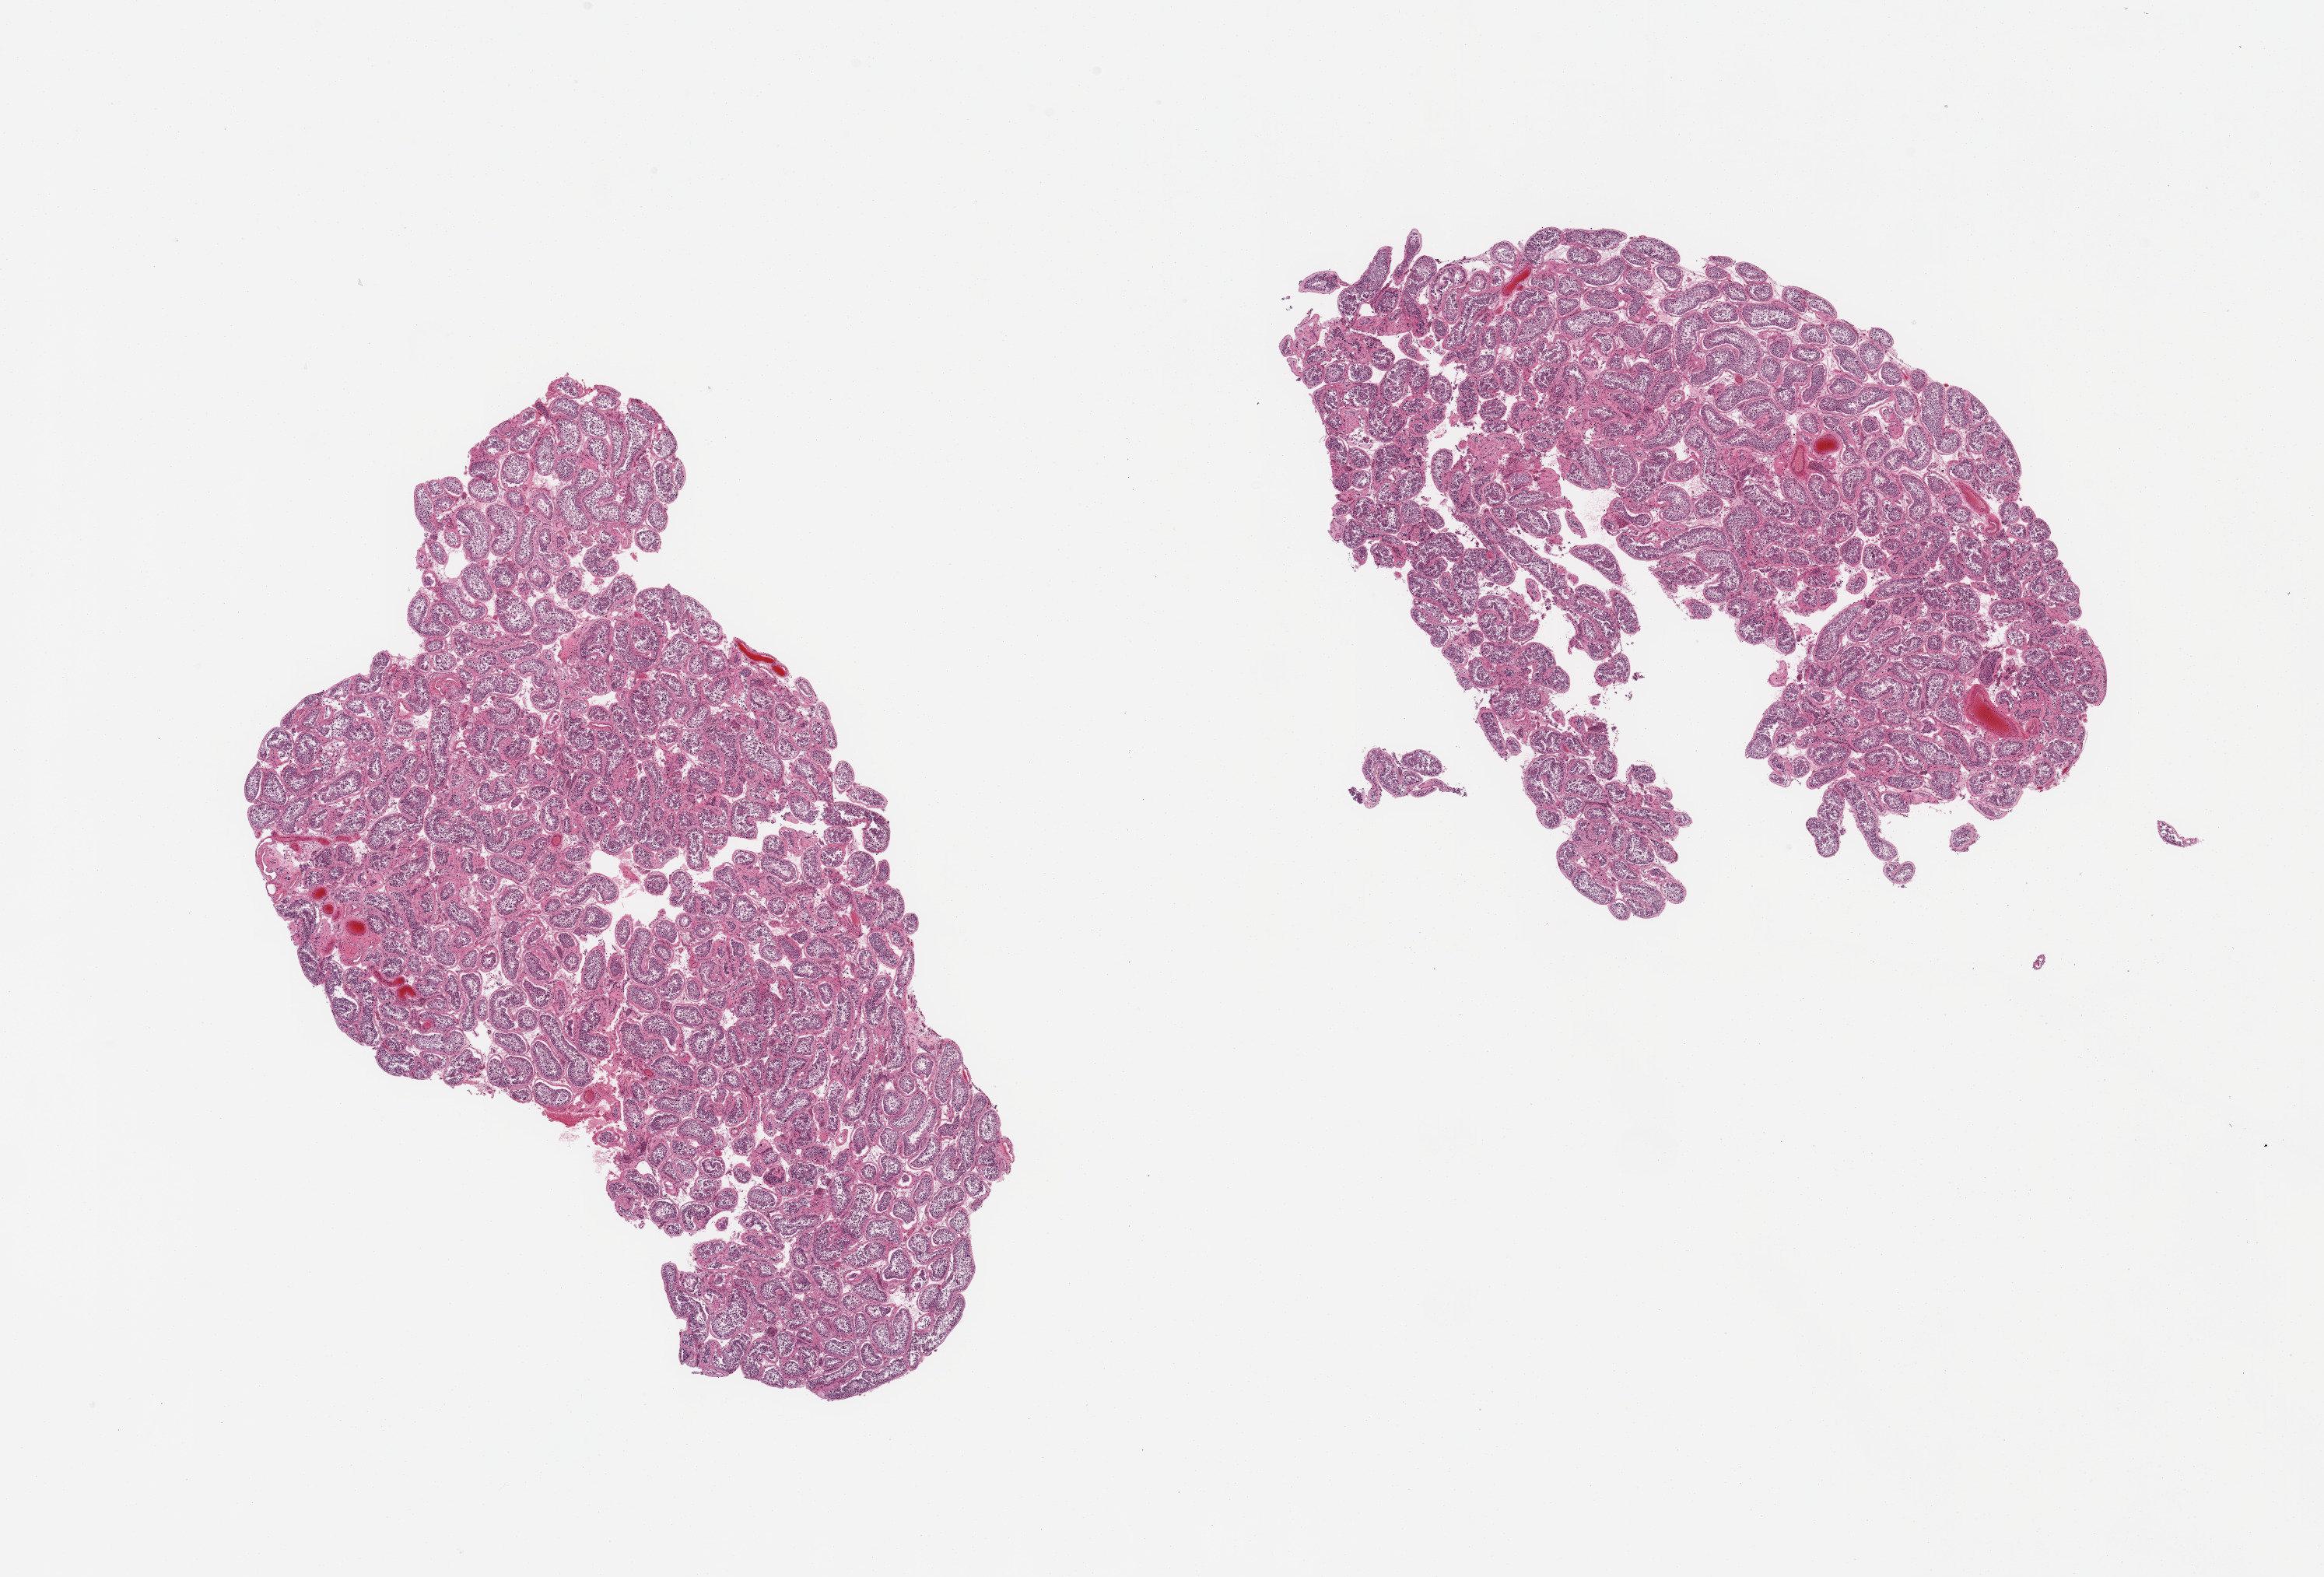
Digitized haematoxylin and eosin-stained section, brightfield, shown as a low-resolution overview of the whole scanned area (about 23.6 x 16.0 mm). PAXgene-fixed paraffin-embedded (PFPE) section. Sampled site (target tissue): testis. Tissue donor sample. Donor: male.
Review note (as recorded): 2 pieces; active spermatogenesis.